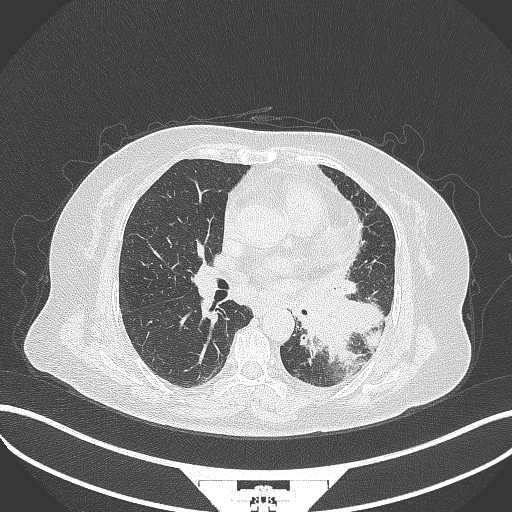
Chest CT, one axial slice. Slice 177 of 322 in the series (ordered by position). 120 kVp. Lung window (W 1500 / L -600 HU). 1 mm slice thickness. 512 × 512 image matrix. Female patient, age 69 years. Case-level facts recorded for this patient, not image findings: clinical TNM (as recorded): T2b N3 M1.
Outlined on this slice (bounding box drawn by a radiologist):
- lung tumour (recorded histology: adenocarcinoma): bounding box <296,287,382,364> (left, top, right, bottom; pixels)